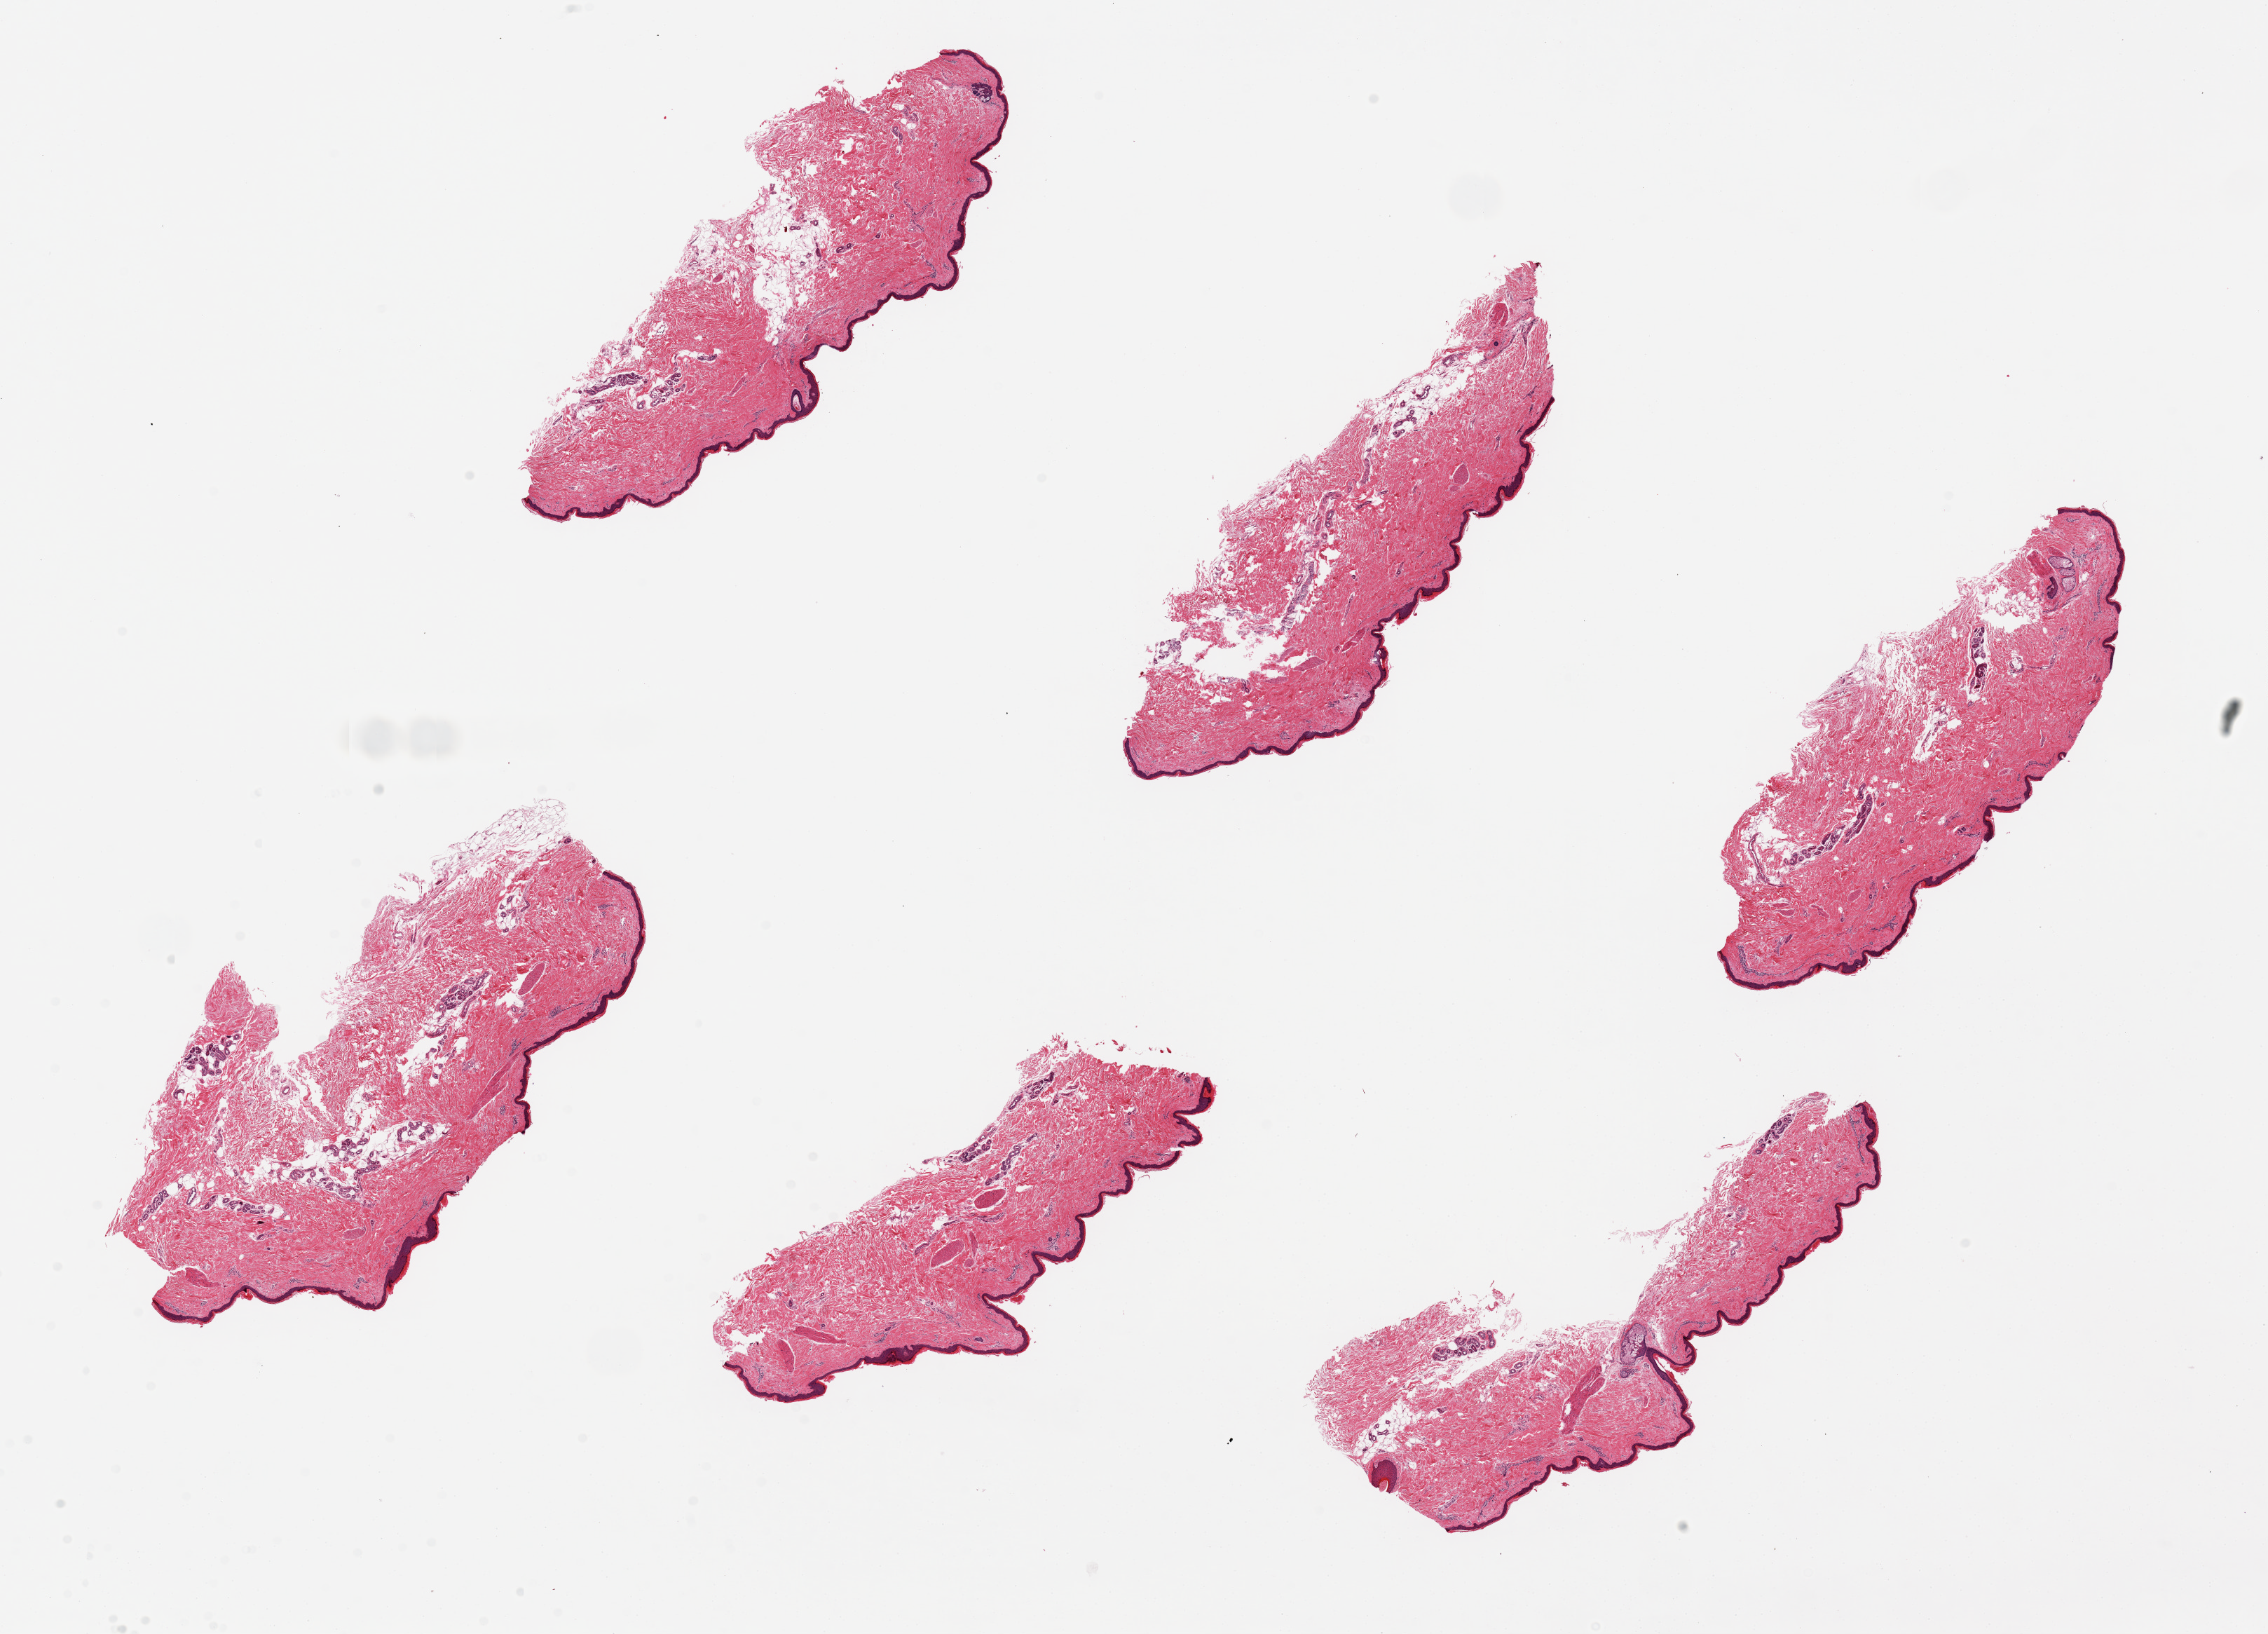
Whole-slide image, H&E stain, a low-resolution overview of the entire scanned area, about 25.6 x 18.4 mm (slide scanned at 20x). PAXgene-fixed paraffin-embedded (PFPE) section. Target tissue: skin of lower leg. Tissue donor sample. Male donor.
• pathologist's review note for this sample: 6 pieces, up to 7x4mm; well dissected